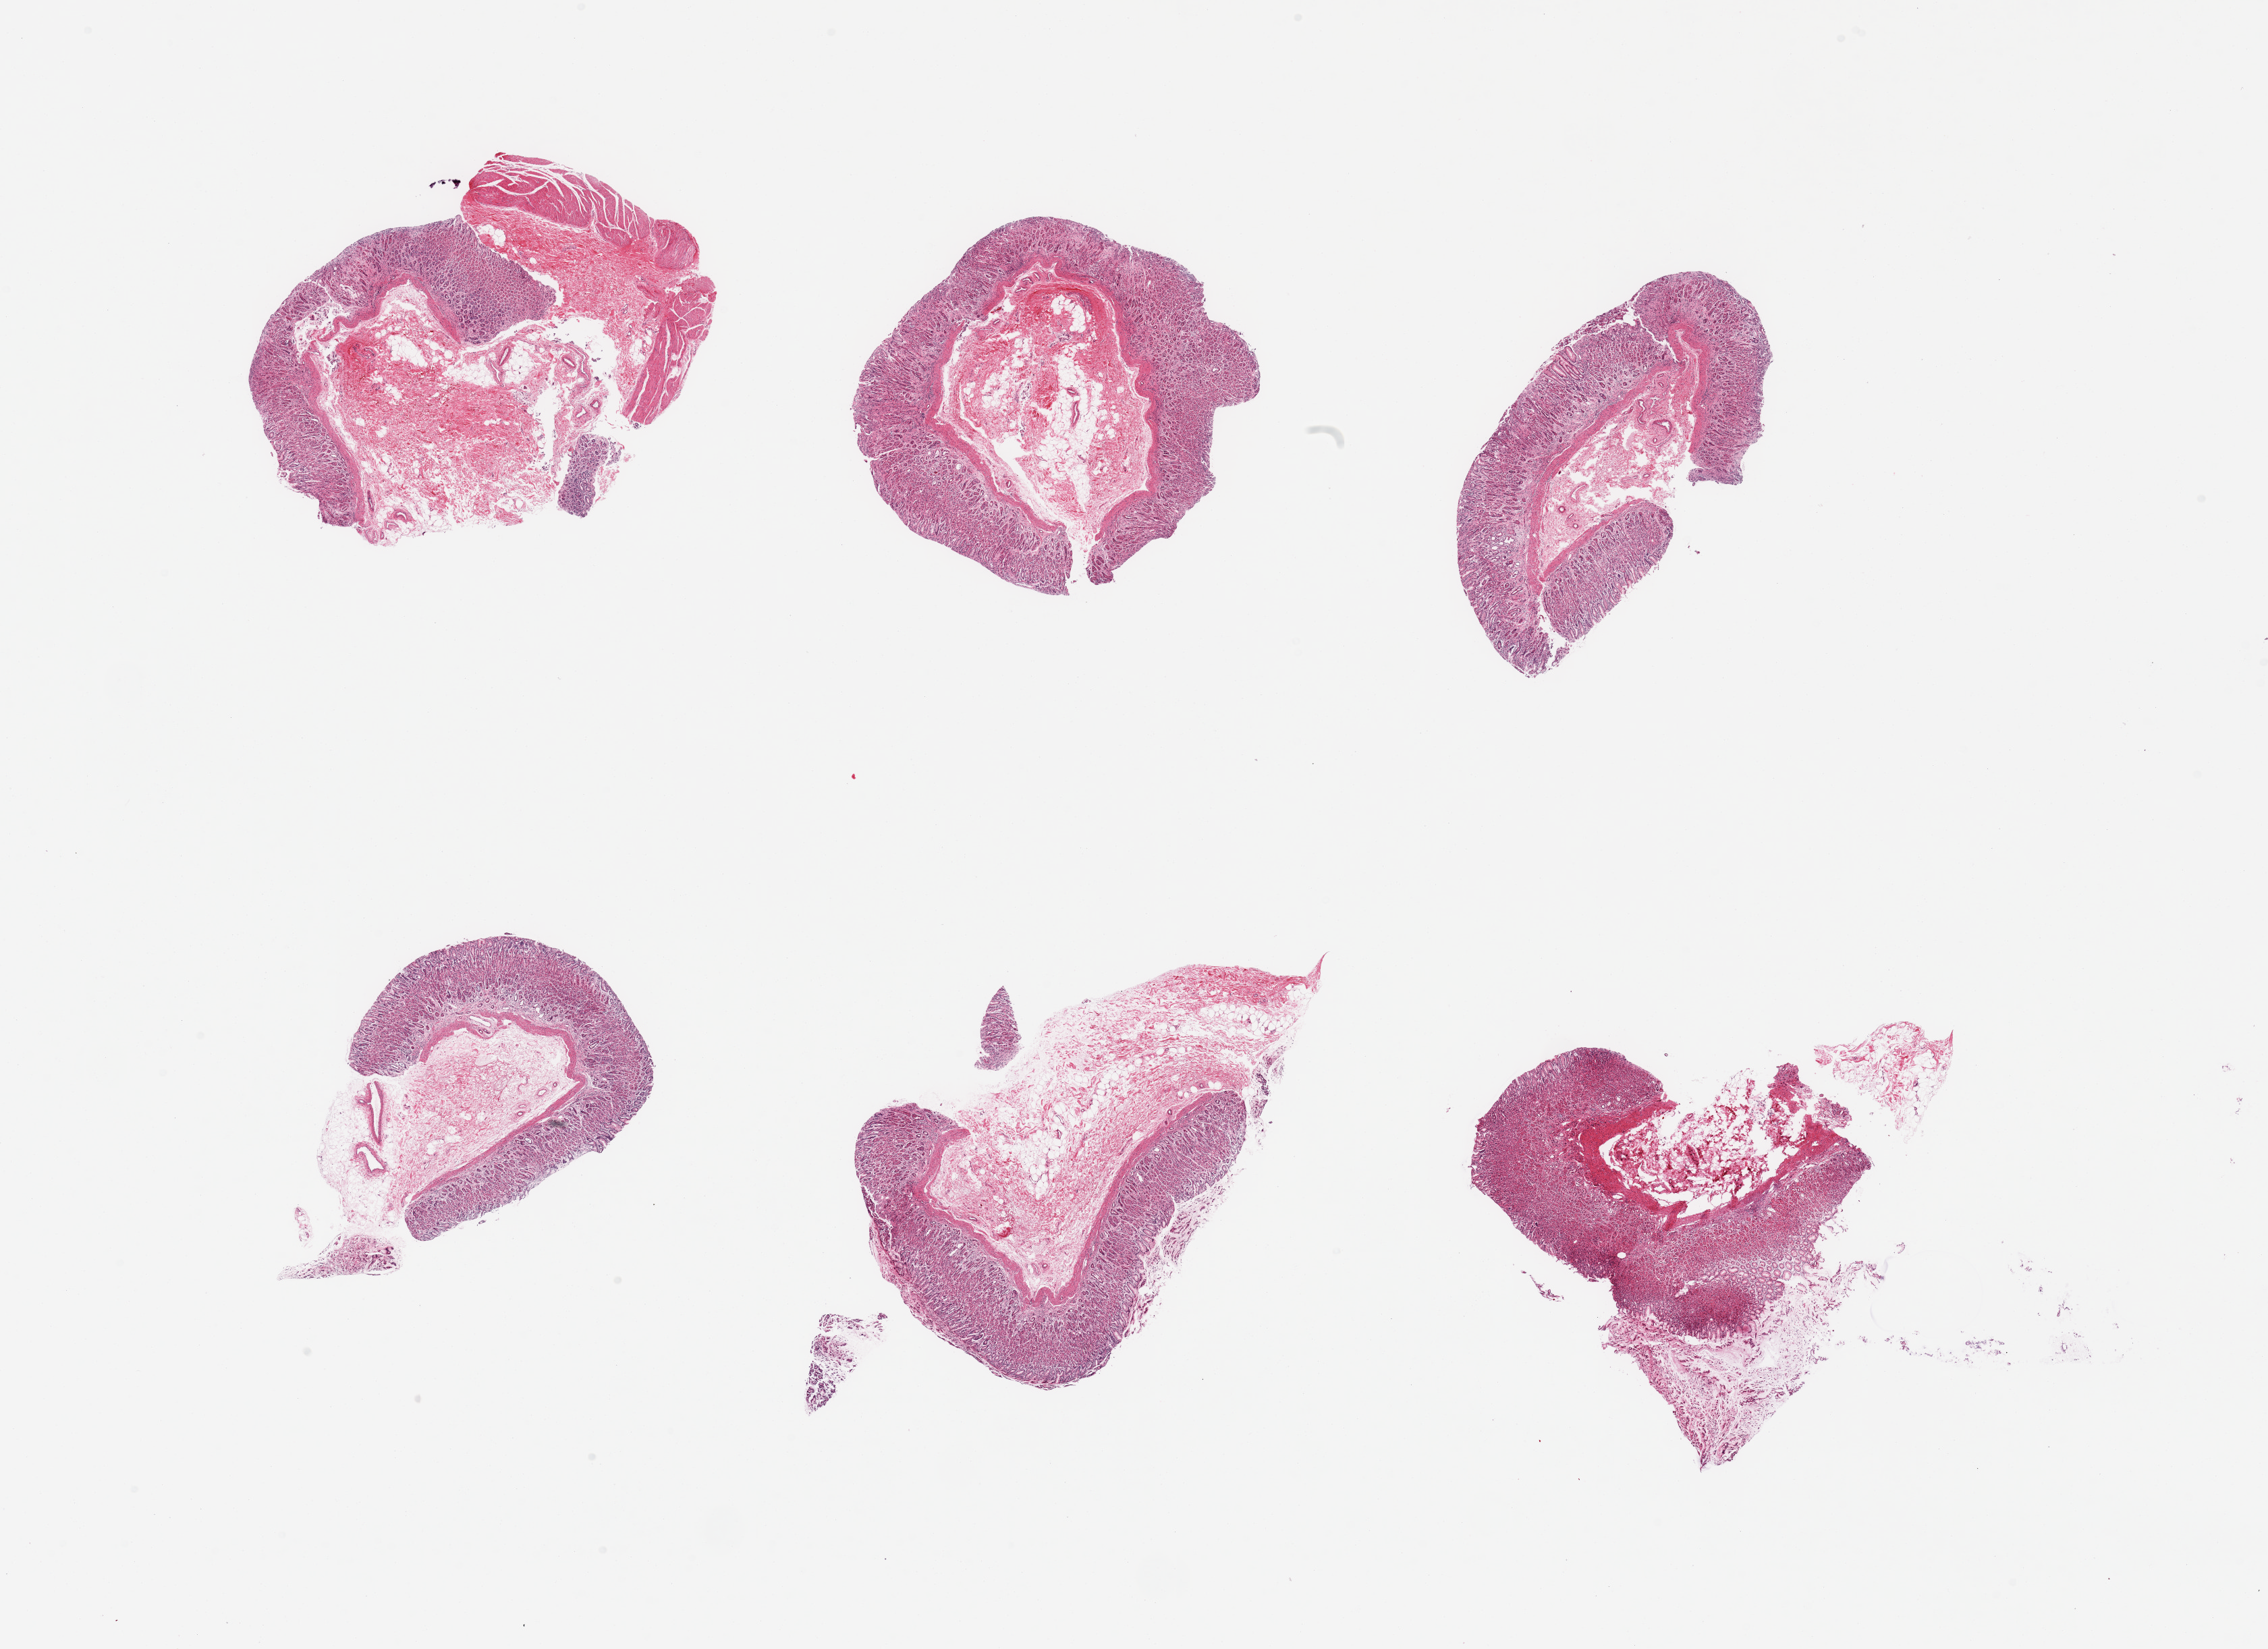
Haematoxylin and eosin whole-slide image — a low-resolution overview of the entire scanned area, about 26.6 x 19.3 mm (acquisition: 20x scan); PAXgene-fixed paraffin-embedded (PFPE) section; target tissue: stomach; donor tissue sample. Donor: male.
Review note (as recorded): 6 pieces, mucosa up to ~1mm, moderately advanced autolysis.